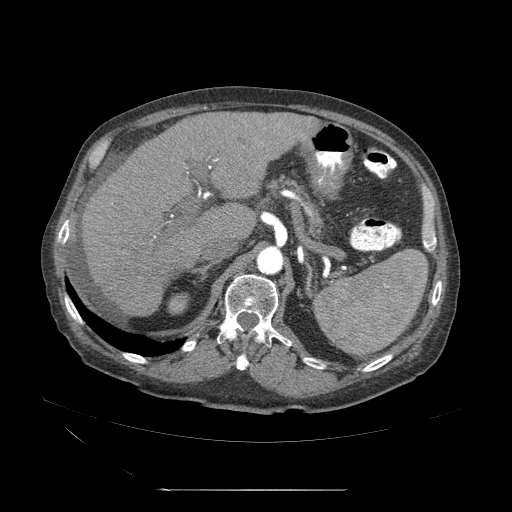
Contrast-enhanced abdominal CT (liver protocol), one axial slice; slice 29 of 71 in the series (ordered by position); 120 kVp; soft-tissue window (W 400 / L 40 HU); 2.5 mm slice thickness; 512 × 512 image matrix, field of view 440 × 440 mm. Case-level facts recorded for this patient, not image findings: diagnosis: hepatocellular carcinoma (patient treated with transarterial chemoembolisation; whether this scan precedes or follows treatment is not stated here); TNM stage (as recorded): Stage-II; Child-Pugh class: A.
Annotated regions visible in this slice (semi-automatically segmented with operator editing):
- abdominal aorta: bounding box (x1, y1, x2, y2) in pixels: (257, 246, 284, 275)
- liver parenchyma outside the tumour (the mass and vessels are separate outlines, so this box may not span the whole liver): (80, 113, 318, 321)
- liver vessels: (141, 161, 239, 264)